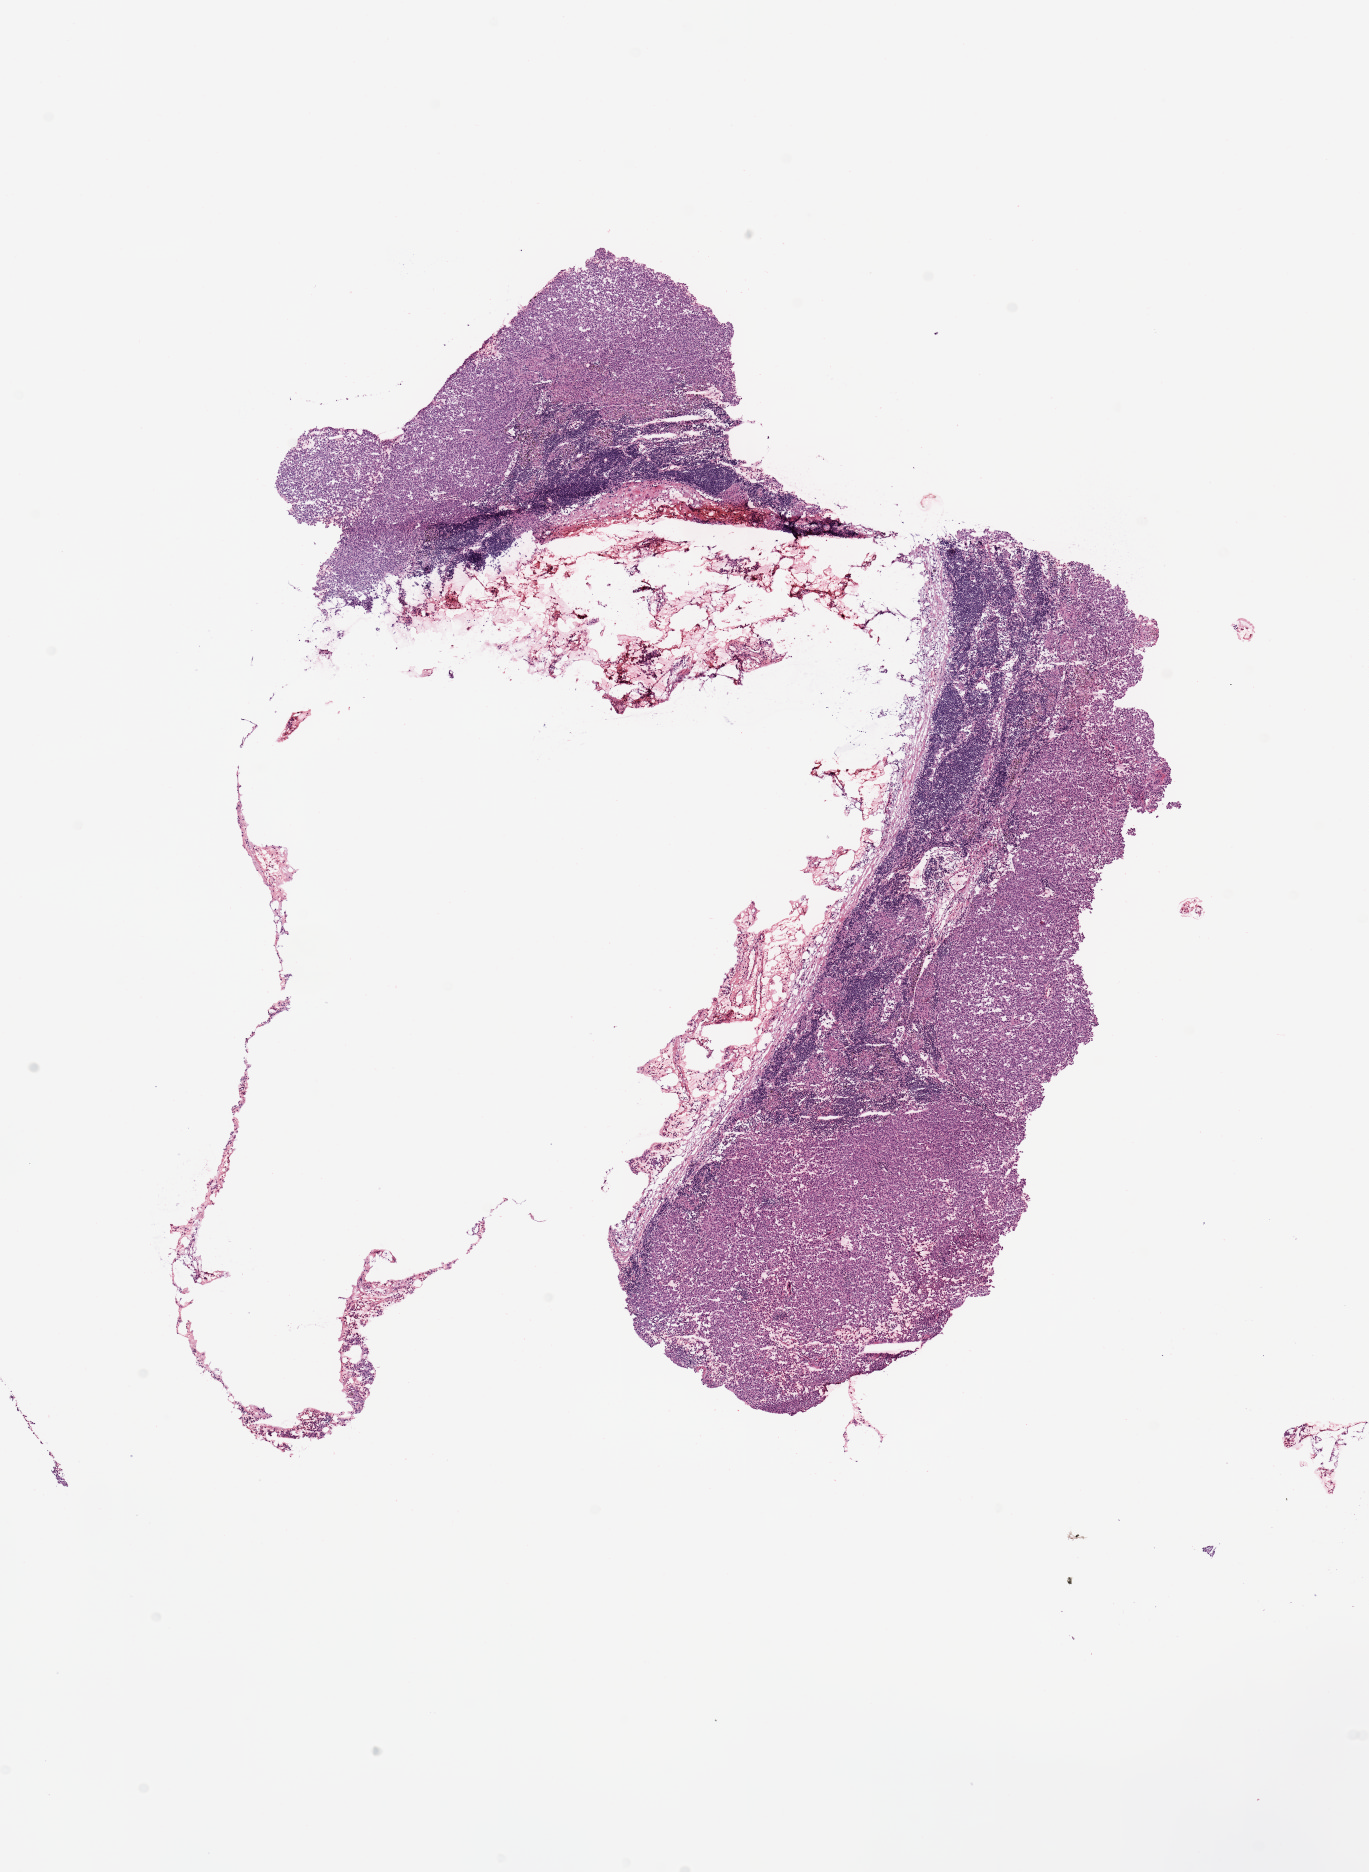
Digitized Hematoxylin and eosin (H&E) stained tissue section (whole slide) — whole scanned area (about 10.8 x 14.8 mm) shown as a low-resolution overview; melanoma tumour tissue; sampled site not recorded. Patient: male, age 51 years.
Patient diagnosis (cohort enrolment): cutaneous melanoma (skin).